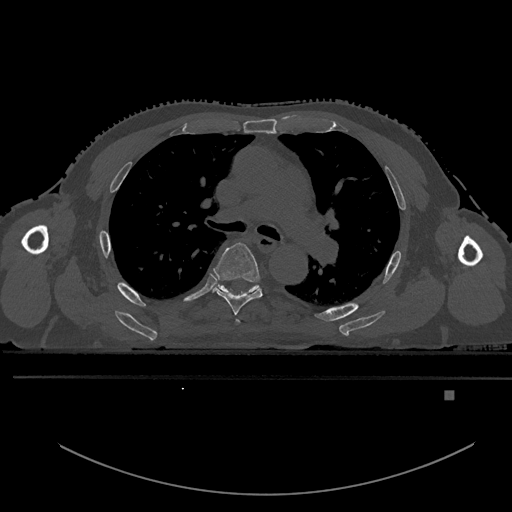
CT including the spine, one axial slice; slice 350 of 969 in the series (ordered by position); bone window (W 1800 / L 400 HU); 0.5 mm slice thickness; 512 × 512 image matrix. Male patient, age 82 years. Case-level facts recorded for this patient, not image findings: primary cancer: prostate; vertebrae with lytic lesions (as recorded): T11, T9, T8, T2.
Structures marked on this image (semi-automatic segmentation, software-assisted and operator-edited):
- T4 vertebra: bounding box <236,319,240,323> (left, top, right, bottom; pixels)
- T5 vertebra: <212,242,263,315>
- T6 vertebra: <212,284,259,294>